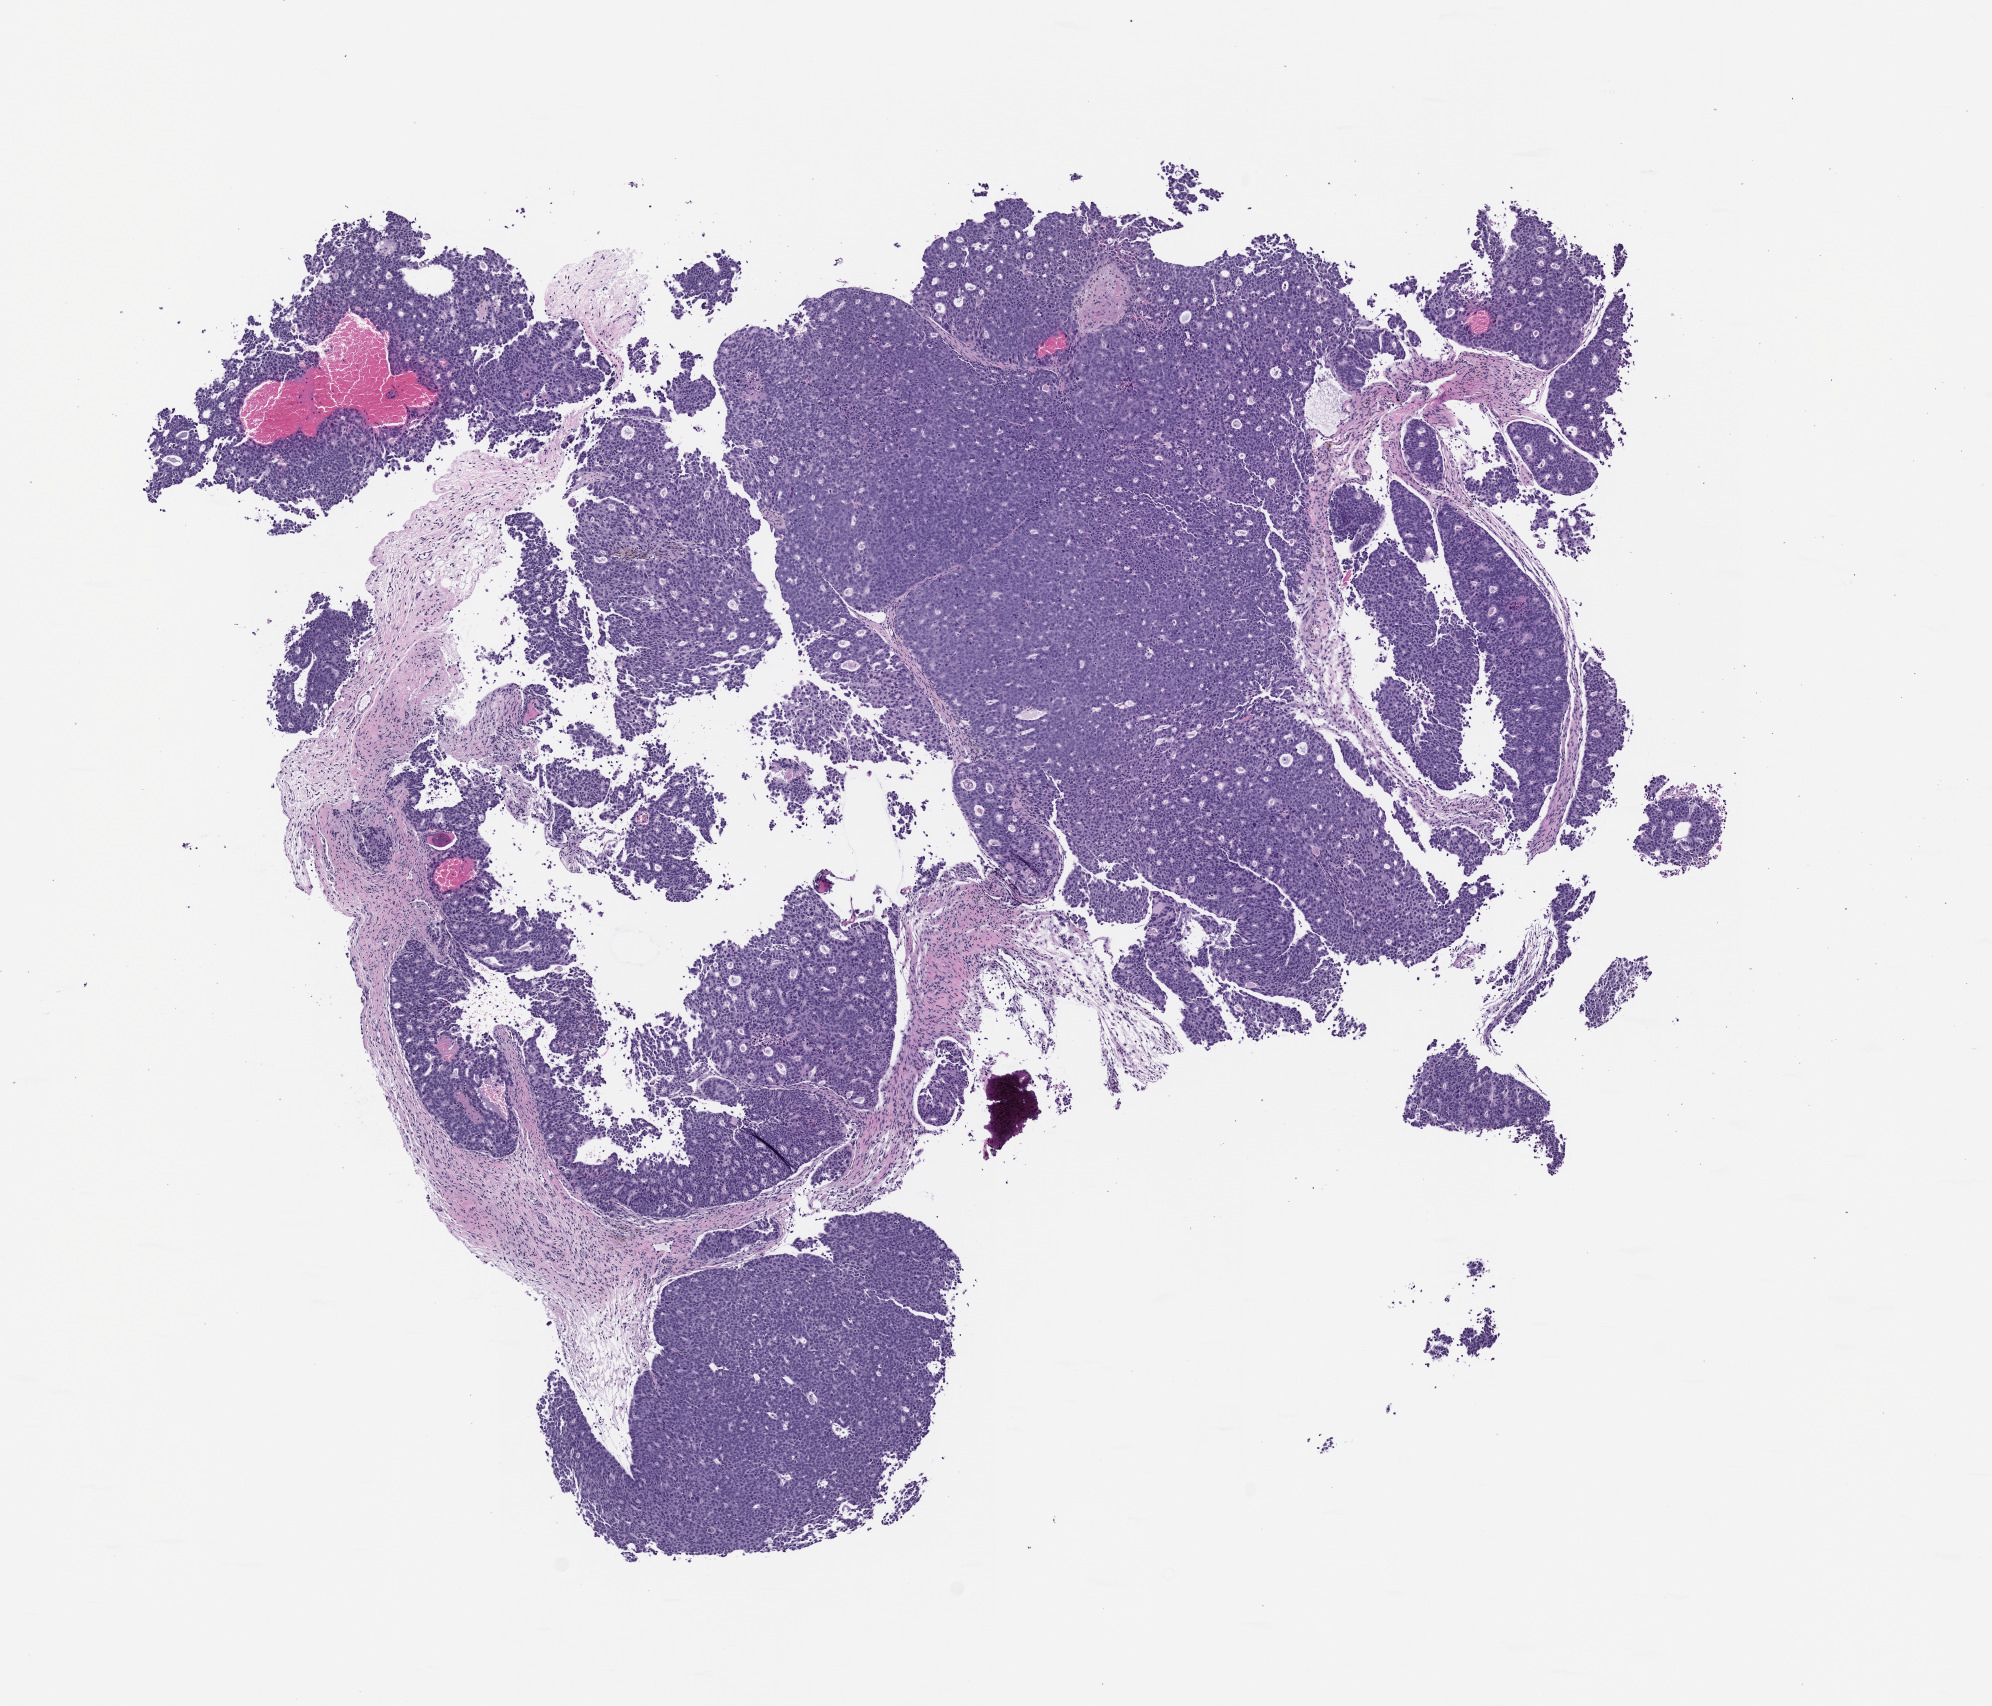
Hematoxylin and eosin (H&E) whole-slide image of a patient-derived xenograft (PDX) tumor grown in a mouse, passage 0 — whole scanned area (about 8.0 x 6.9 mm) shown as a low-resolution overview. FFPE section. Originating tumor site category: colon.
Originating patient diagnosis: Colon Adenocarcinoma.